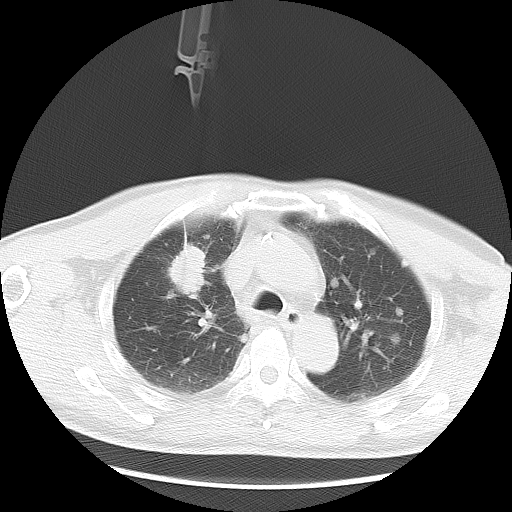
Chest CT, one axial slice; position 21 of 35 along the scan axis; reconstruction kernel LUNG; lung window (W 1500 / L -600 HU); 512 × 512 image matrix. Male patient, age 57 years. From the clinical record (not read from this slice): clinical TNM (as recorded): T2 N3 M1a.
Outlined on this slice (bounding box drawn by a radiologist):
- lung tumour (recorded histology: adenocarcinoma): bounding box [x1, y1, x2, y2] px = [165, 242, 209, 298]